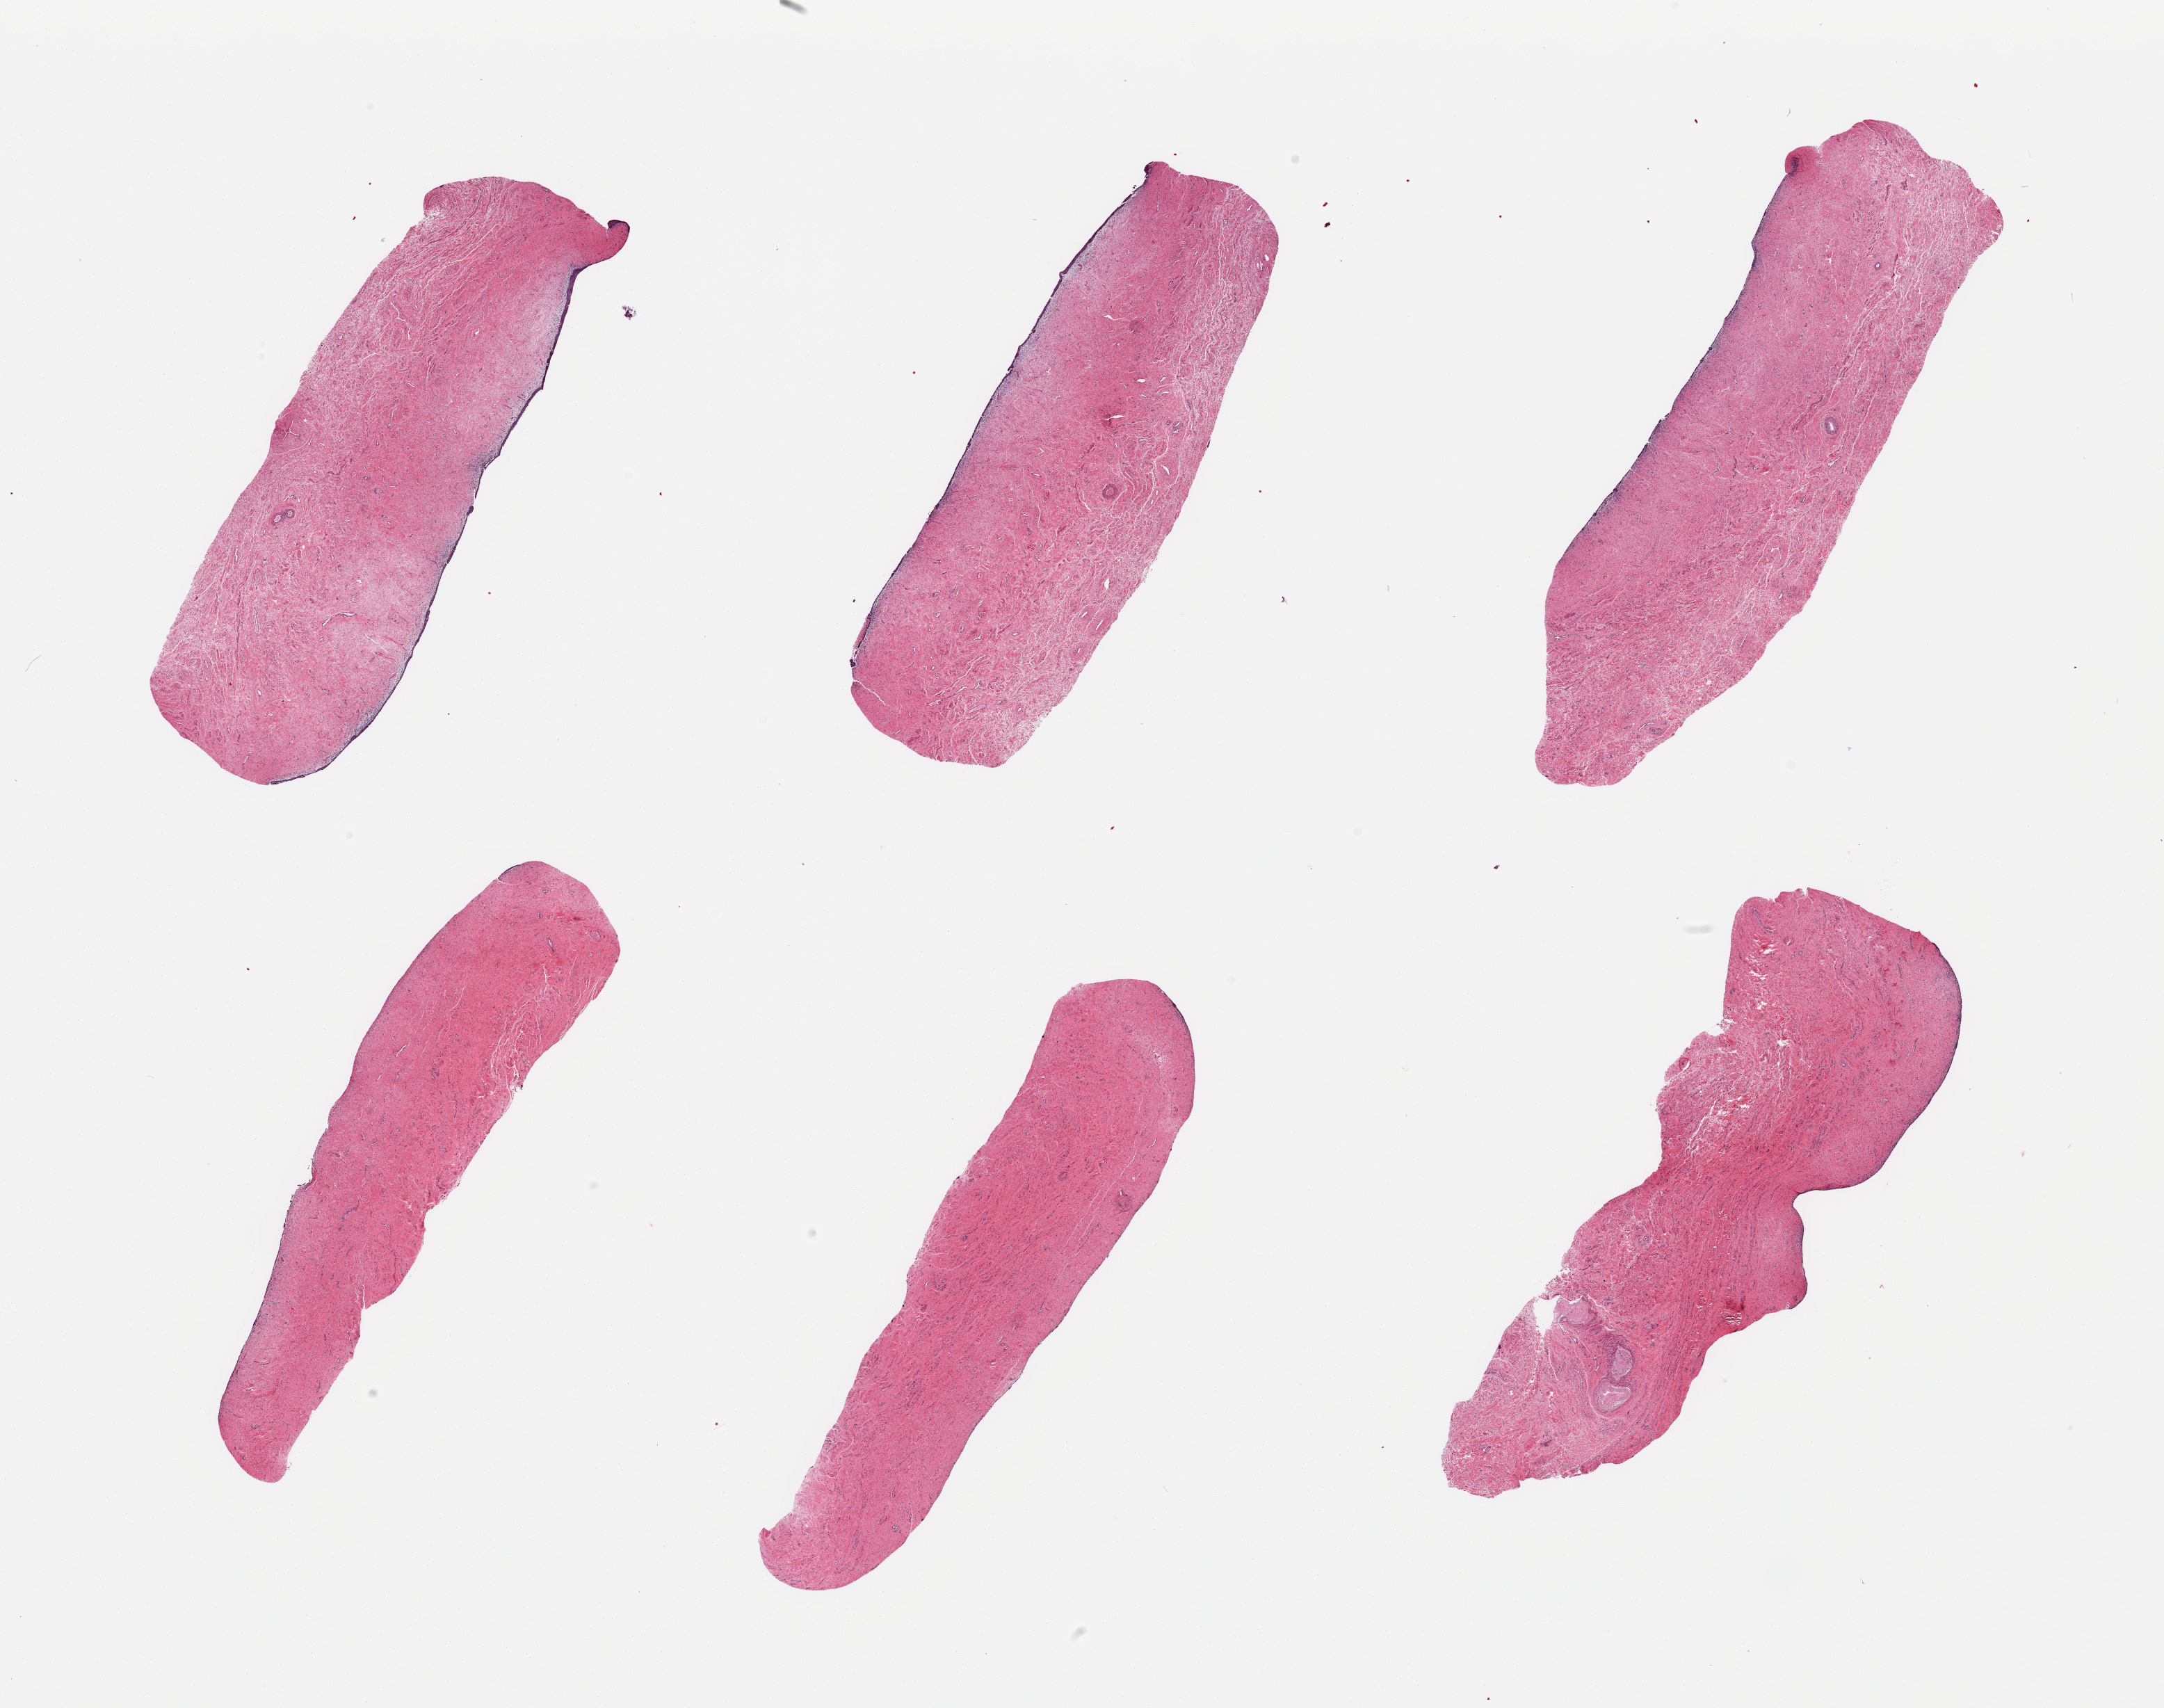
Digitized haematoxylin and eosin-stained section — low-resolution overview of the scanned area, about 24.6 x 19.4 mm (acquisition: 20x scan); PAXgene-fixed paraffin-embedded (PFPE) section; section of vagina (target tissue); donor tissue sample. Female donor.
Pathologist's review note for this sample: 6 pieces, squamous mucosa is sloughing, where residual, ~38 microns.